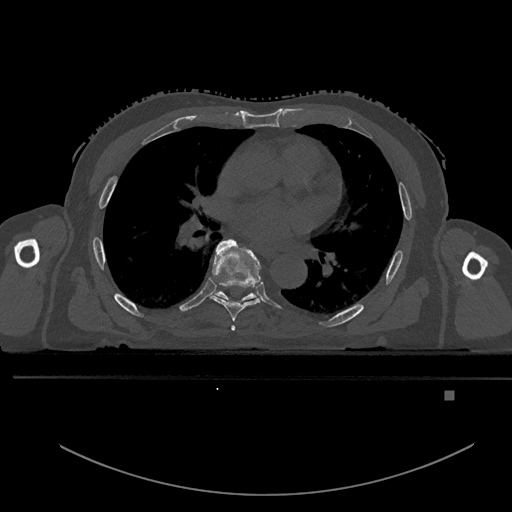
CT including the spine, one axial slice; slice 289 of 969 in the series (ordered by position); bone window (W 1800 / L 400 HU); 0.5 mm slice thickness; 512 × 512 image matrix, field of view 456 × 456 mm. Patient: male, 82 years. From the clinical record (not read from this slice): primary cancer: prostate; vertebrae with lytic lesions (as recorded): T11, T9, T8, T2.
Annotated regions visible in this slice (semi-automatically segmented with operator editing):
- T5 vertebra: box from (x=231, y=325) to (x=236, y=331) px
- T6 vertebra: (x=210, y=239)–(x=261, y=321)
- T7 vertebra: (x=214, y=291)–(x=256, y=300)